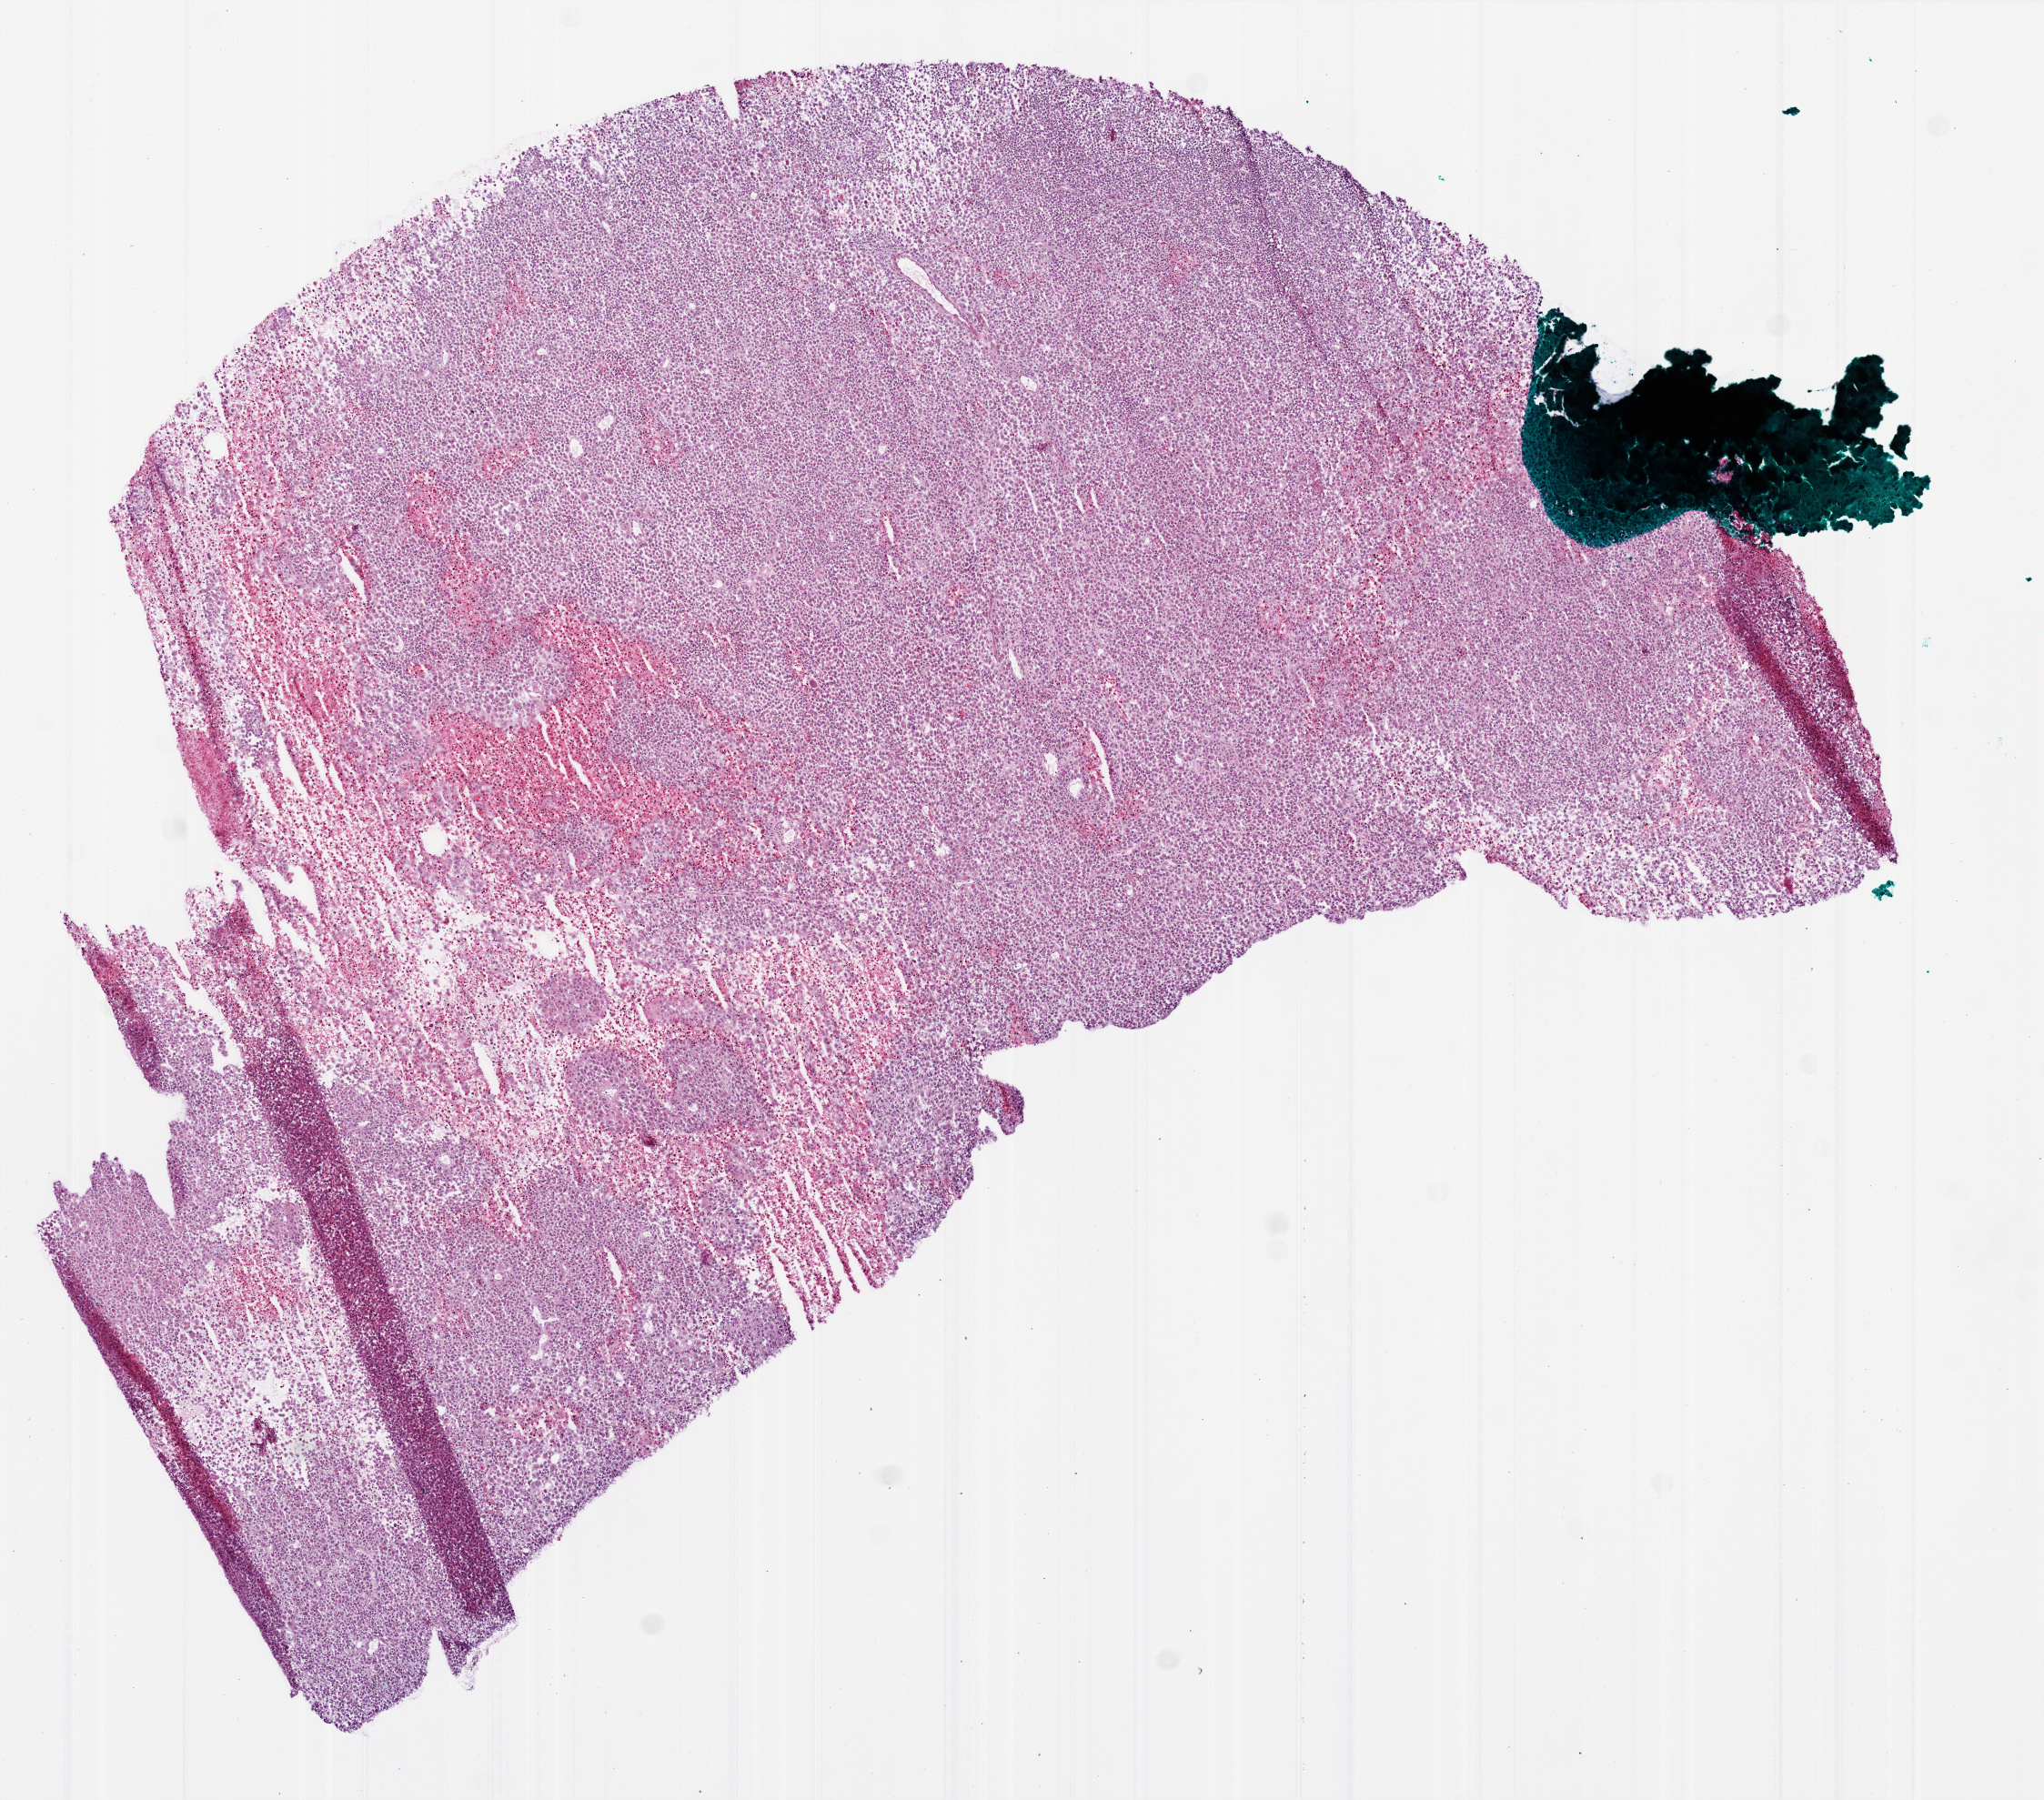
Digitized Hematoxylin and eosin (H&E) stained tissue section (whole slide), shown as a low-resolution overview of the whole scanned area (about 9.0 x 7.9 mm, acquisition: 20x scan); frozen section from the bottom of the tissue portion; primary tumour sample from the brain. Male patient; age at initial diagnosis 60 years. Composition of this section per pathologist review: tumour cells 80%, tumour nuclei 100%, normal cells 0%, stromal cells 0%, necrosis 20%.
Histologic diagnosis: Glioblastoma.